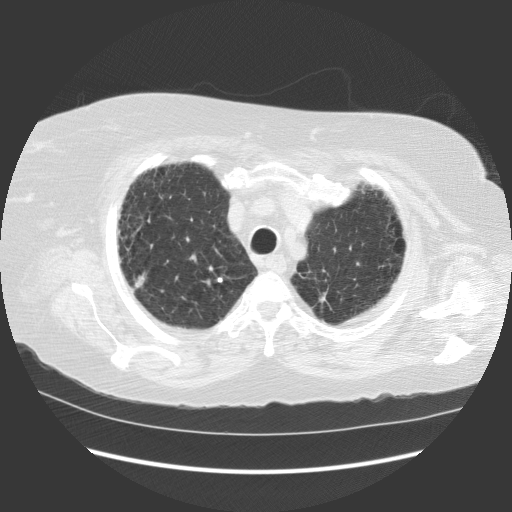
Low-dose screening chest CT, one axial slice. Position 100 of 121 along the scan axis. Reconstruction kernel STANDARD. 140 kVp. Lung window (W 1500 / L -600 HU). 512 × 512 image matrix, field of view 380 × 380 mm.
Outlined on this slice (manually delineated by an expert):
- lesion 1 (tumor, upper lobe of right lung): box from (x=135, y=274) to (x=145, y=288) px